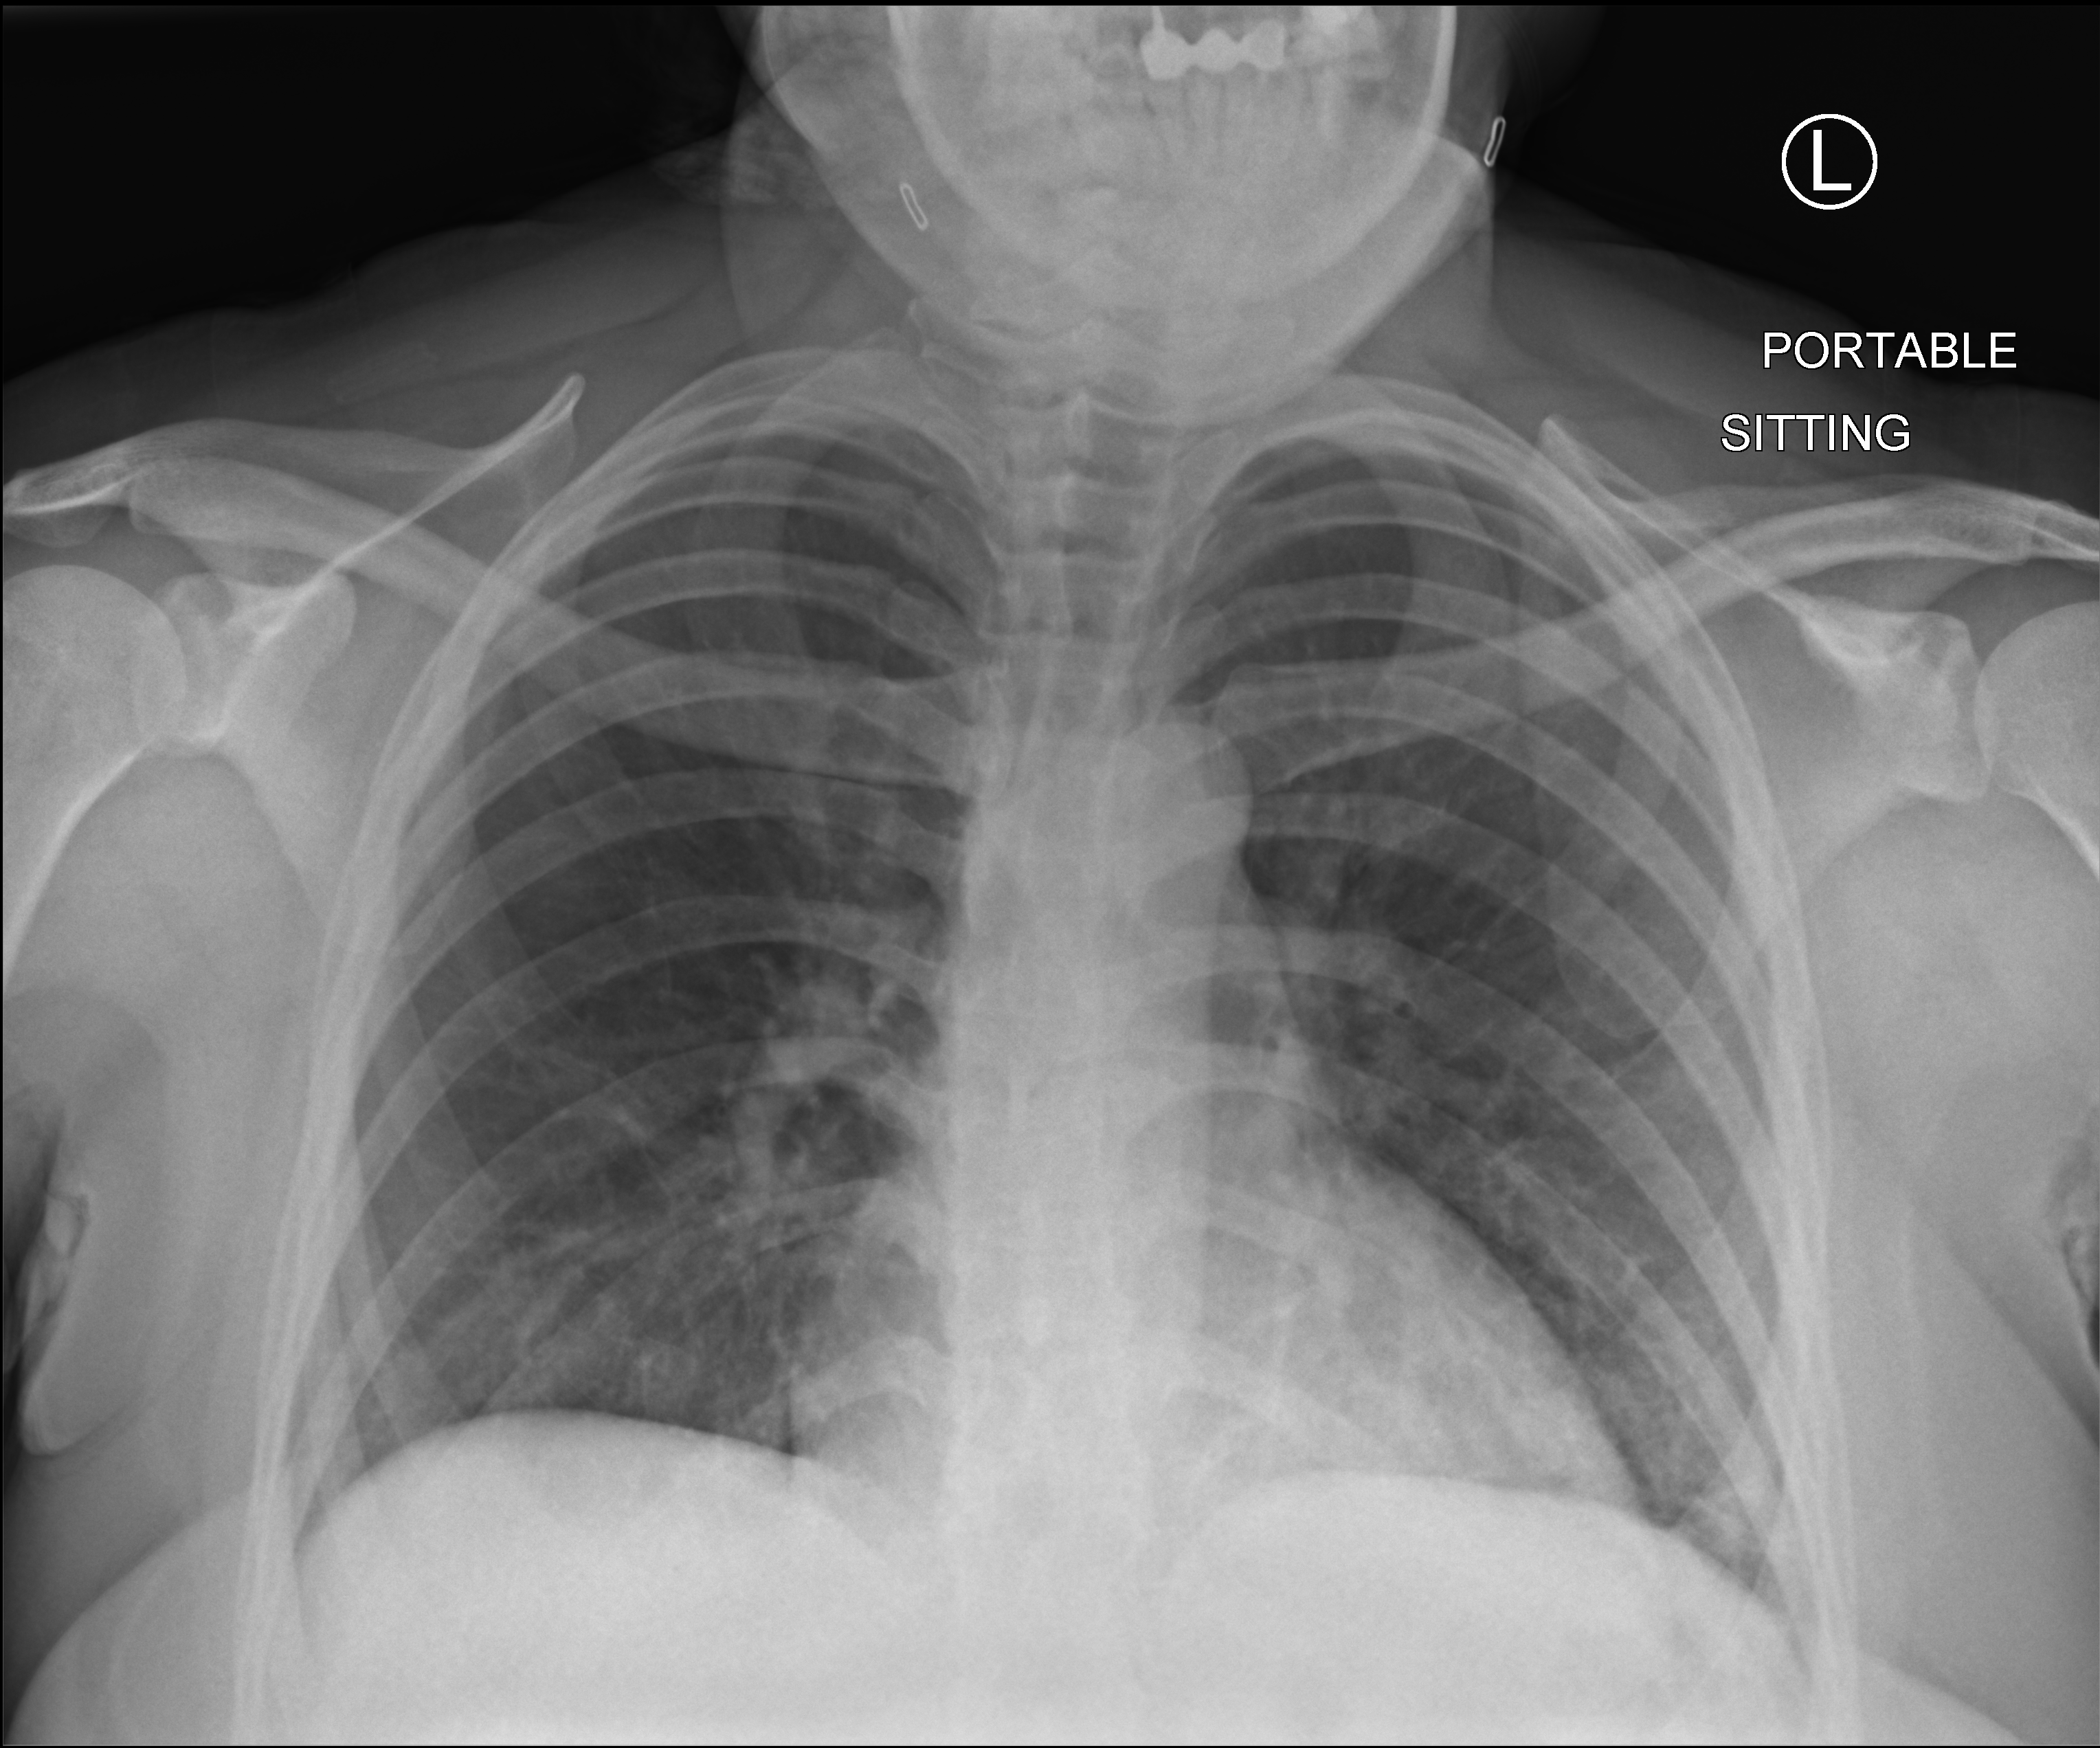
Portable chest radiograph, anteroposterior (AP) projection. Female patient hospitalised with COVID-19, age 18–59 years.
Admission-level facts for this patient (not findings on this image; timing relative to this image not recorded): chronic kidney disease (admission record): no.